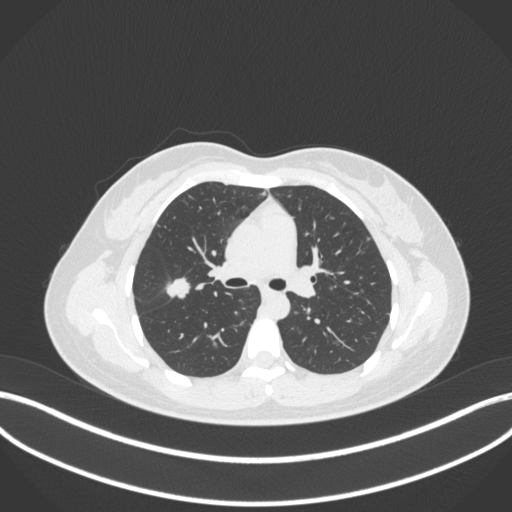
Chest CT, one axial slice; reconstruction kernel B31f; 120 kVp; lung window (W 1500 / L -600 HU); 1 mm slice thickness; 512 × 512 image matrix, field of view 400 × 400 mm. Patient: female, 33 years. From the clinical record (not read from this slice): clinical TNM (as recorded): T1c N0 M0; histopathological grade: G2-G3.
Annotated regions visible in this slice (rectangle marked by the reading radiologist):
- lung tumour (recorded histology: adenocarcinoma): bounding box [x1, y1, x2, y2] px = [163, 271, 190, 304]